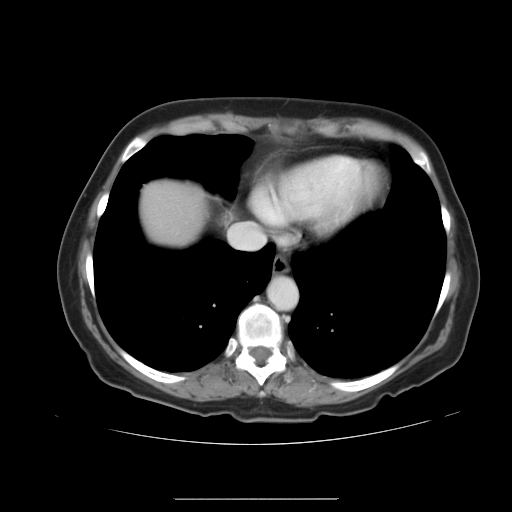
Contrast-enhanced abdominal CT, one axial slice. Slice 36 of 41 in the series (ordered by position). Intravenous contrast given. Soft-tissue window (W 400 / L 40 HU). 512 × 512 image matrix. Female patient, age 63 years. From the clinical record (not read from this slice): diagnosis: colorectal cancer liver metastases, imaged before liver resection; multiple liver metastases: yes; largest metastasis: 1.5 cm; chemotherapy before resection: no.
Structures marked on this image (expert manual segmentation):
- liver: bounding box <141,179,207,247> (left, top, right, bottom; pixels)
- planned liver remnant (the part of the liver to remain after resection): <141,179,207,248>